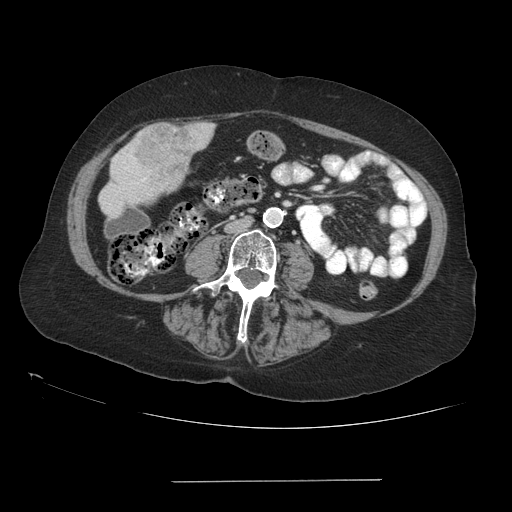
Contrast-enhanced abdominal CT (liver protocol), one axial slice. Slice 17 of 89 in the series (ordered by position). 140 kVp. Soft-tissue window (W 400 / L 40 HU). 2.5 mm slice thickness. 512 × 512 image matrix. Case-level facts recorded for this patient, not image findings: diagnosis: hepatocellular carcinoma (patient treated with transarterial chemoembolisation; whether this scan precedes or follows treatment is not stated here); TNM stage (as recorded): Stage-IVA; Child-Pugh class: A; tumour nodularity: uninodular.
Structures marked on this image (semi-automatically segmented with operator editing):
- liver parenchyma outside the tumour (the mass and vessels are separate outlines, so this box may not span the whole liver): bounding box [x1, y1, x2, y2] px = [98, 132, 199, 218]
- mass: [129, 121, 215, 190]